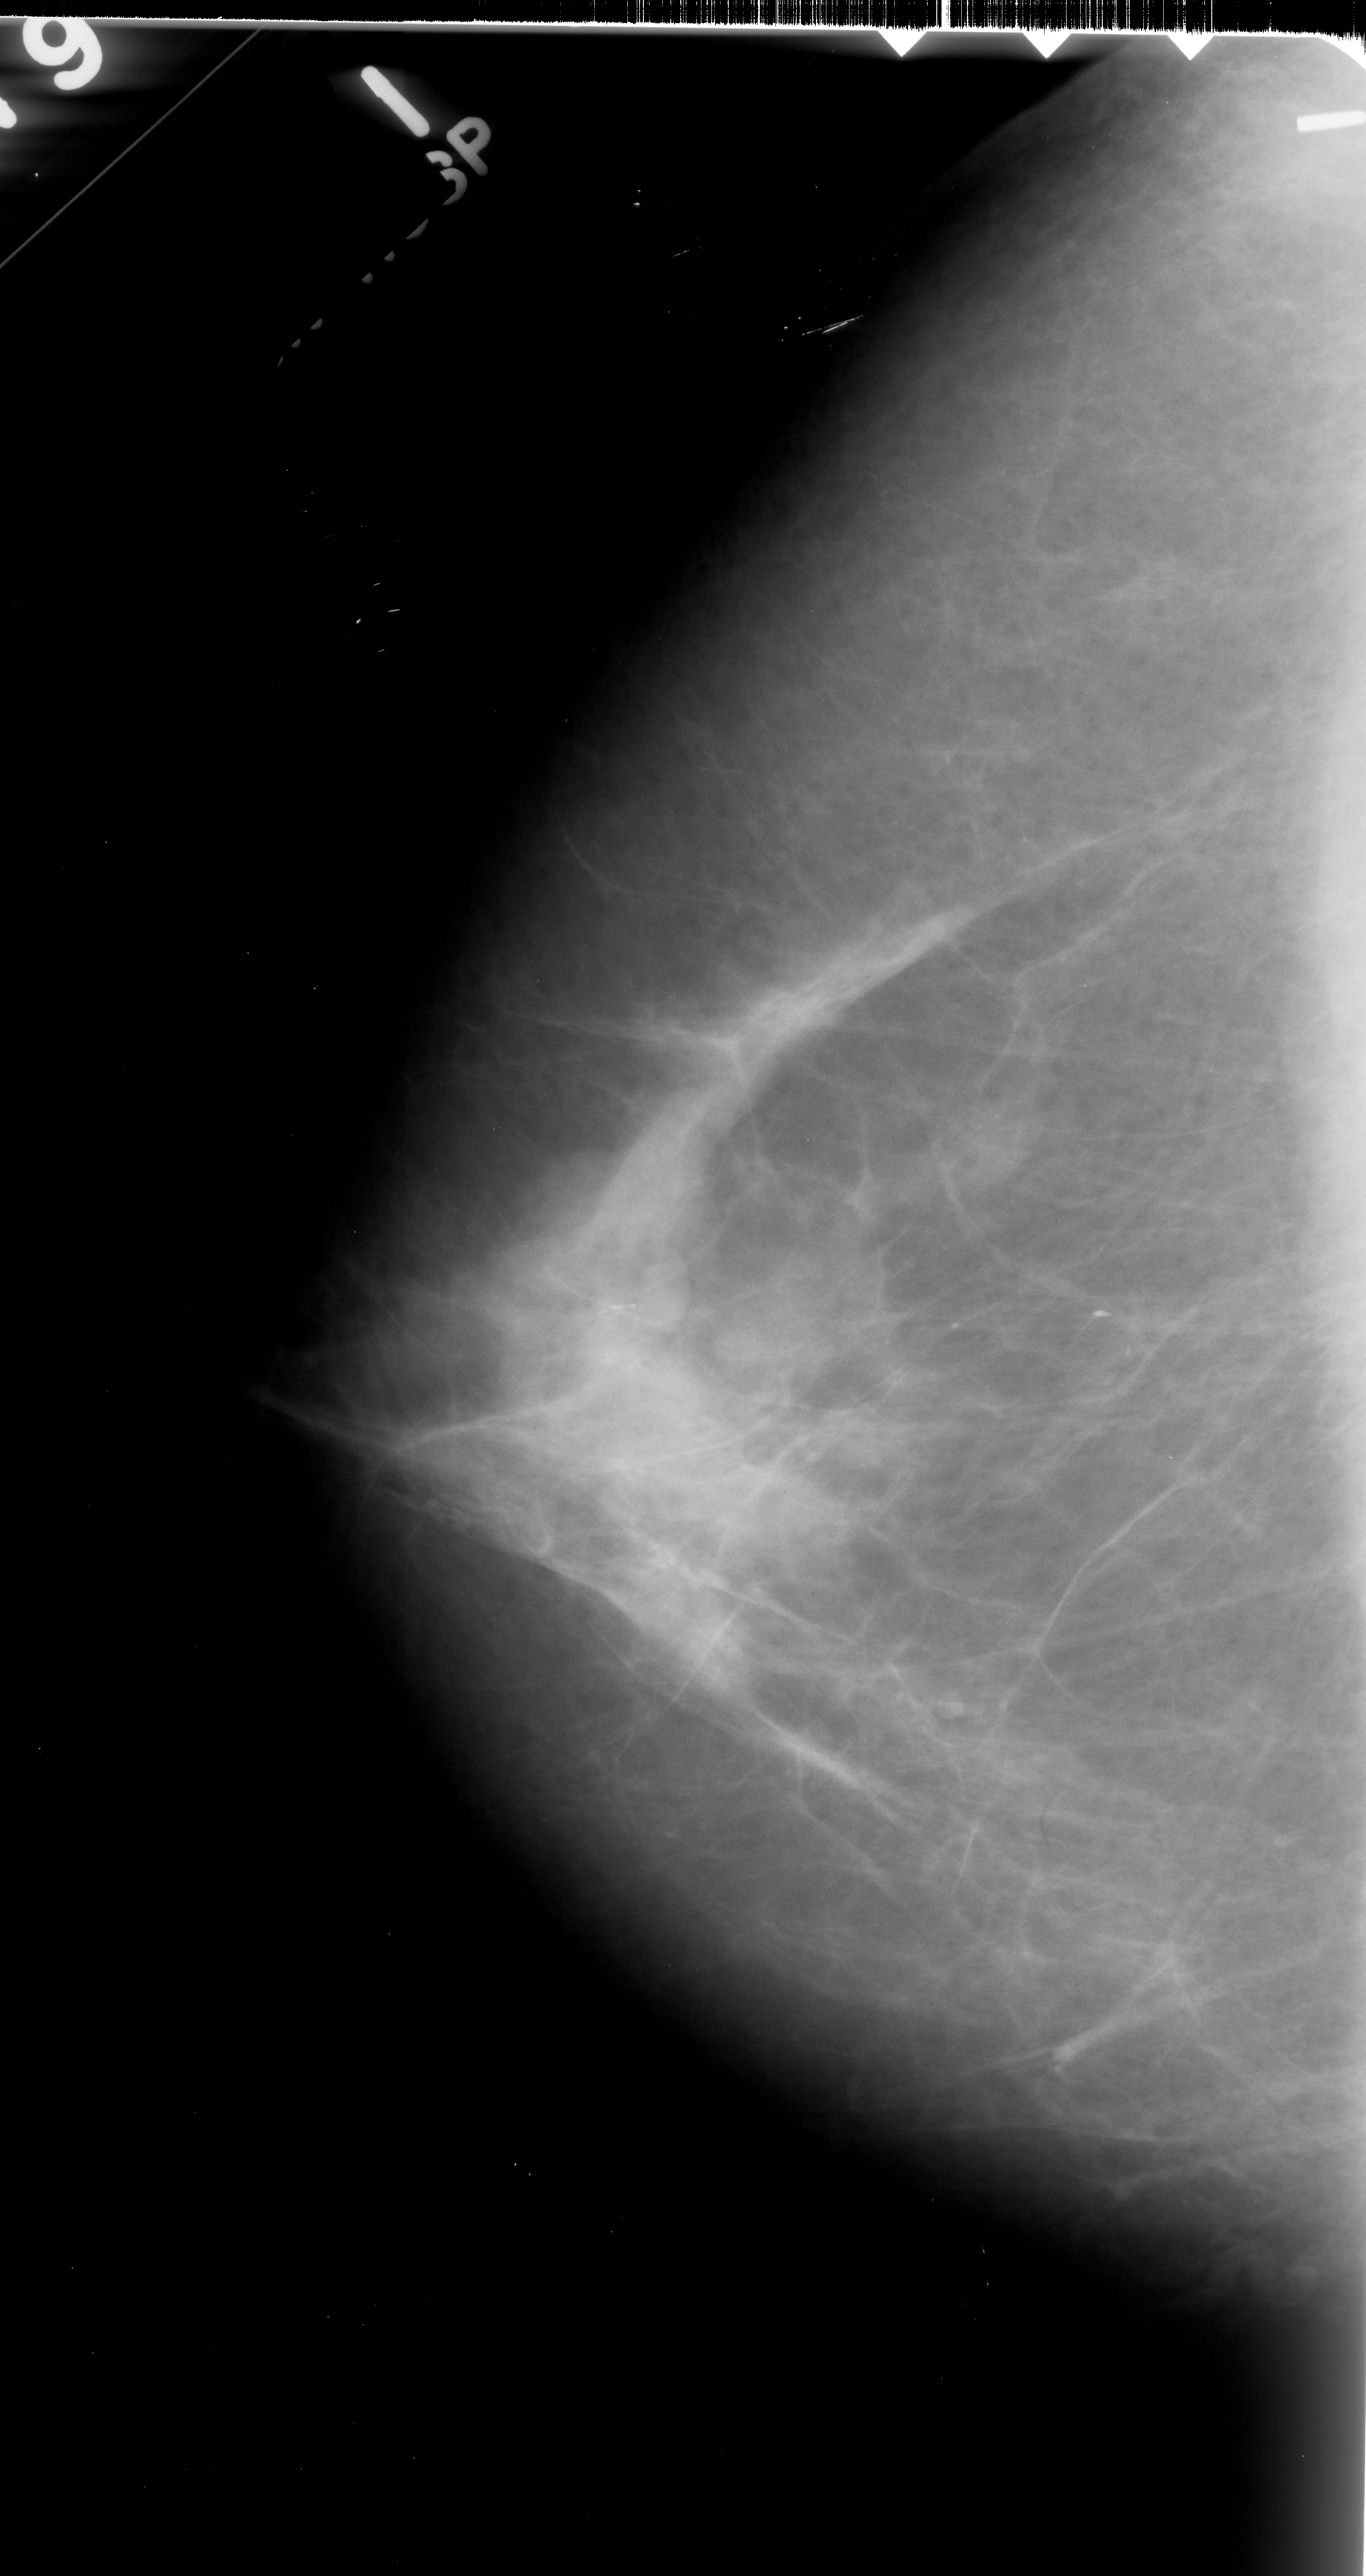
Mammogram (digitized film), left breast, craniocaudal (CC) view, breast composition: scattered fibroglandular densities (BI-RADS density category 2 of 4).
Abnormality record for this image: calcifications, morphology fine linear branching, distribution linear; BI-RADS assessment category 4; subtlety rating 2 on a 1 (subtle) to 5 (obvious) scale; pathology (as recorded): malignant.